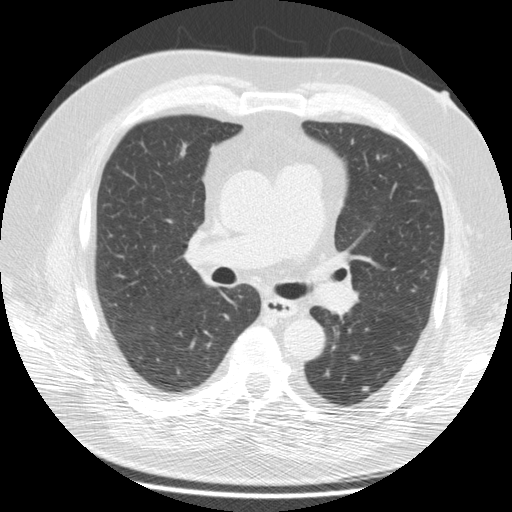
Chest CT (low-dose screening protocol), one axial image, third annual screen, lung window (W 1500 / L -600 HU), 2.5 mm slice thickness, standard (soft-tissue) reconstruction kernel (STANDARD), 120 kVp, slice 70 of 172 in the series, 512 × 512 image matrix, field of view 364 × 364 mm. Male participant, aged 69 years at enrolment. Former smoker at enrolment.
• Expert reader's lesion annotation, box from (x=353, y=372) to (x=382, y=400) px.
• The screening reader recorded 2 non-calcified nodules or masses ≥4 mm on this exam (left lower lobe, left lower lobe); which of them this box marks is not recorded.
• Official screen result: positive, other.
• Participant outcome: lung cancer diagnosed 224 days after this screen — squamous cell carcinoma, NOS, left lower lobe, moderately differentiated (G2), stage IA (AJCC 6th edition), 14 mm at pathology.